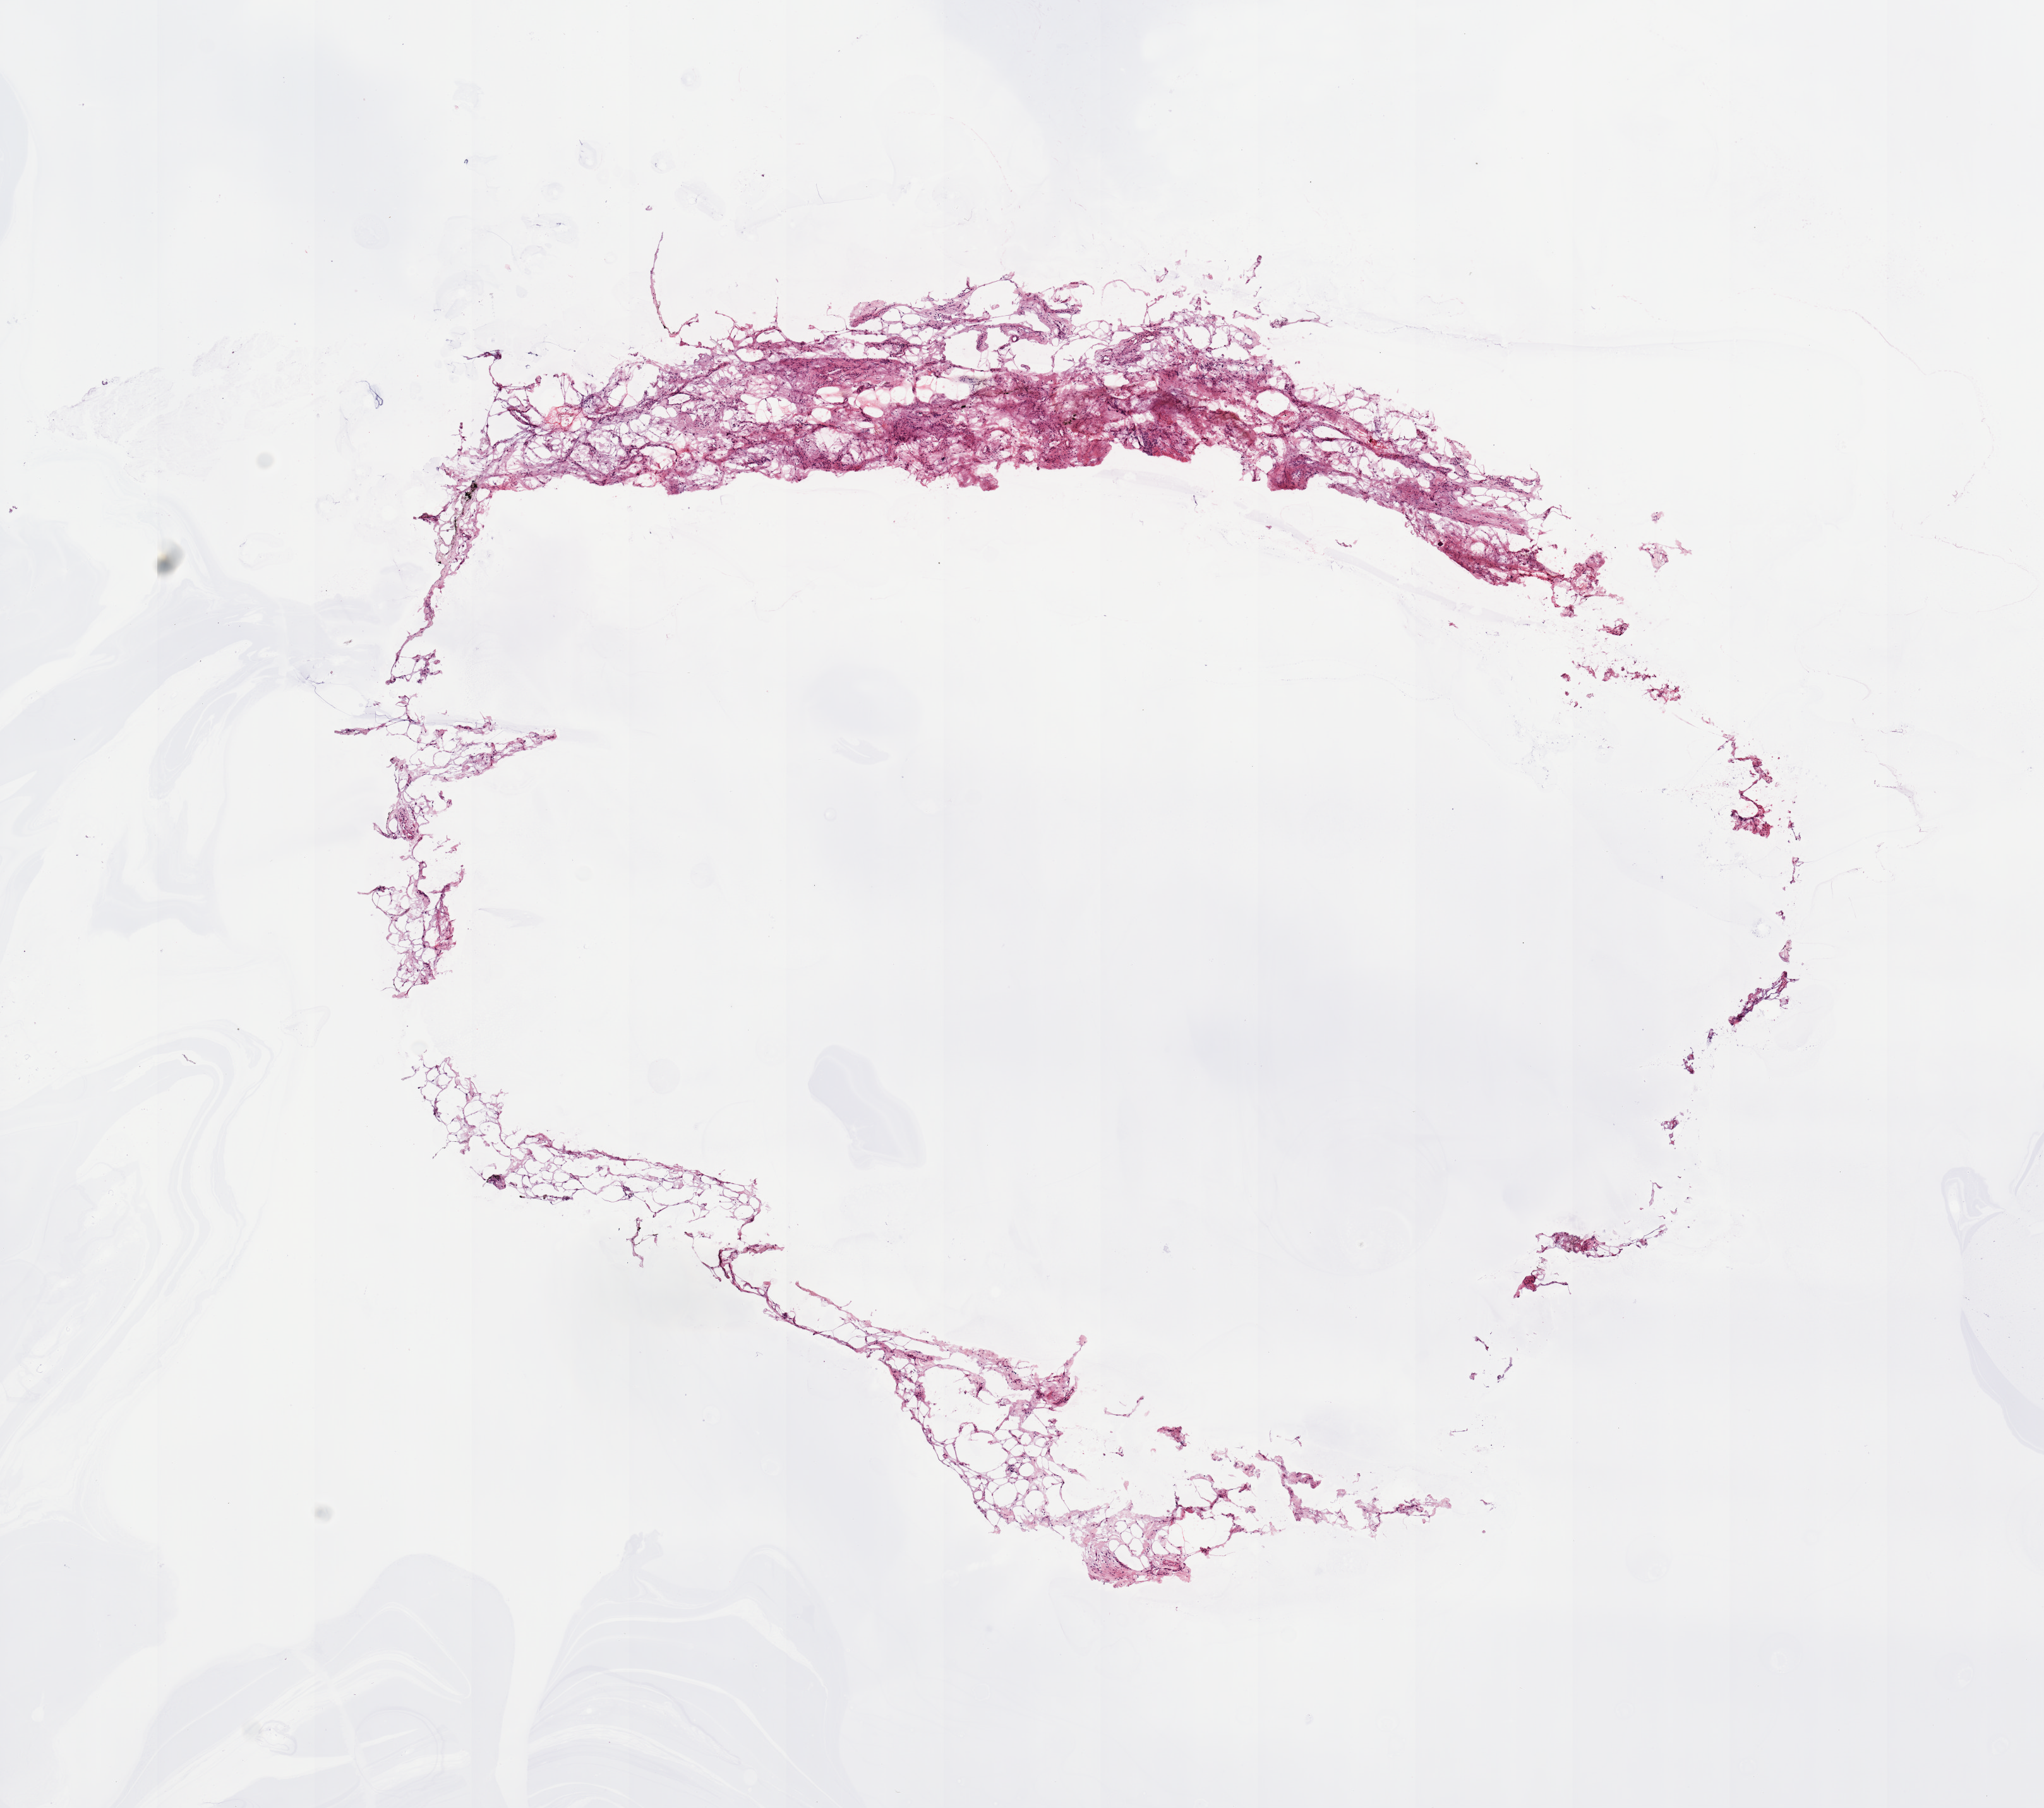
H&E whole-slide image — whole scanned area (about 12.8 x 11.3 mm, slide scanned at 20x) shown as a low-resolution overview, pancreas, normal (non-tumour) tissue. 59-year-old female patient.
This section: normal (non-tumour) tissue from the same patient. Patient diagnosis: Infiltrating duct carcinoma, NOS.